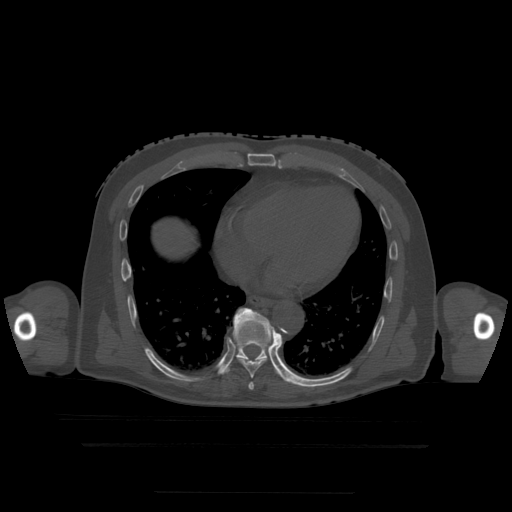
CT including the spine, one axial slice. Position 272 of 522 along the scan axis. Bone window (W 1800 / L 400 HU). 1.25 mm slice thickness. 512 × 512 image matrix, field of view 436 × 436 mm. Patient age 68 years. Case-level facts recorded for this patient, not image findings: primary cancer: urothelial.
Annotated regions visible in this slice (semi-automatic segmentation, software-assisted and operator-edited):
- T7 vertebra: bounding box <248,382,254,390> (left, top, right, bottom; pixels)
- T8 vertebra: <240,309,272,379>
- T9 vertebra: <223,308,284,379>